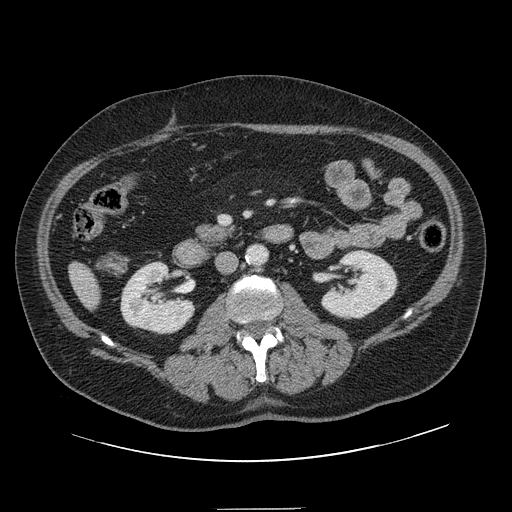
Contrast-enhanced abdominal CT, one axial slice. Position 35 of 154 along the scan axis. 120 kVp. Intravenous contrast given. Soft-tissue window (W 400 / L 40 HU). 2.5 mm slice thickness. 512 × 512 image matrix, field of view 451 × 451 mm. Male patient, age 61 years. From the clinical record (not read from this slice): diagnosis: colorectal cancer liver metastases, imaged before liver resection; multiple liver metastases: yes; largest metastasis: 2.6 cm.
Structures marked on this image (outlined manually by an expert reader):
- liver: bounding box (x1, y1, x2, y2) in pixels: (71, 265, 101, 308)
- planned liver remnant (the part of the liver to remain after resection): (71, 265, 101, 308)